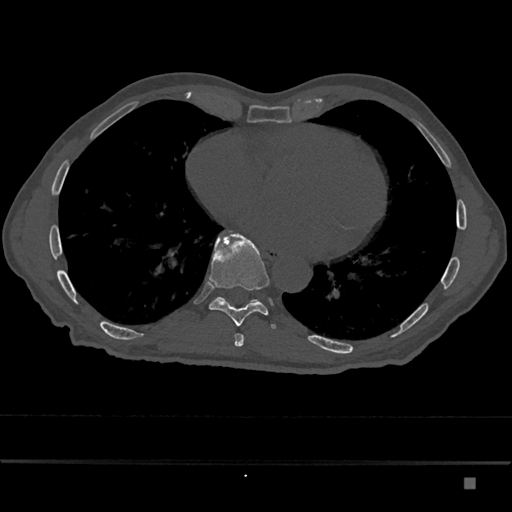
CT including the spine, one axial slice. Slice 795 of 797 in the series (ordered by position). Reconstruction kernel Br40s/3. 120 kVp. Bone window (W 1800 / L 400 HU). 512 × 512 image matrix. Male patient, age 72 years. Case-level facts recorded for this patient, not image findings: primary cancer: prostate.
Annotated regions visible in this slice (semi-automatic segmentation, software-assisted and operator-edited):
- T10 vertebra: bounding box (x1, y1, x2, y2) in pixels: (216, 297, 260, 303)
- T9 vertebra: (209, 231, 276, 329)